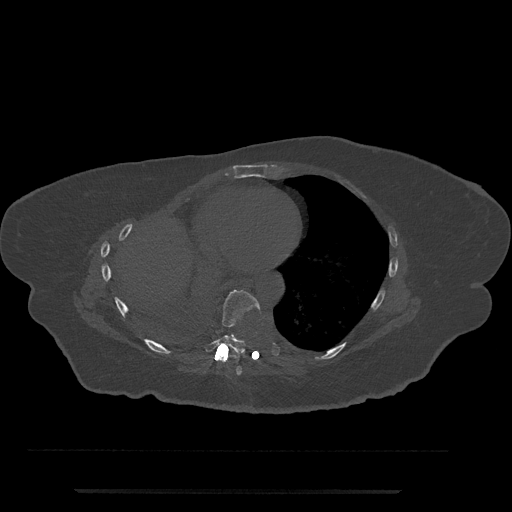
CT including the spine, one axial slice; slice 389 of 797 in the series (ordered by position); bone window (W 1800 / L 400 HU); 0.5 mm slice thickness; 512 × 512 image matrix, field of view 440 × 440 mm. Patient: female, 51 years. Case-level facts recorded for this patient, not image findings: primary cancer: neuro; vertebrae with lytic lesions (as recorded): T8.
Outlined on this slice (semi-automatic segmentation, software-assisted and operator-edited):
- T7 vertebra: bounding box <235,365,242,375> (left, top, right, bottom; pixels)
- T8 vertebra: <204,289,261,353>
- T9 vertebra: <231,334,234,336>